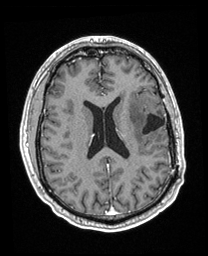
Brain MRI from a brain-tumour surgery series, one axial slice; slice 92 of 208 in the series (ordered by position); T1-weighted post-contrast; 1 mm slice thickness; 208 × 256 image matrix, field of view 211 × 260 mm. From the clinical record (not read from this slice): histopathology: Astrocytoma; WHO grade: 3; IDH mutation: yes.
Outlined on this slice (outlined manually by an expert reader):
- previous resection cavity: bounding box <142,114,165,134> (left, top, right, bottom; pixels)